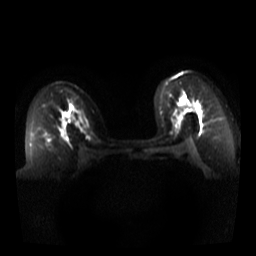
Breast MRI, one axial slice; position 22 of 44 along the scan axis; diffusion-weighted series; image 2 of 4 stored at this slice position (different b-values; order by instance number); 3 T; 5 mm slice thickness; 256 × 256 image matrix, field of view 340 × 340 mm. Female patient.
Structures marked on this image (manually delineated by an expert):
- tumour on diffusion-weighted imaging: box from (x=184, y=100) to (x=199, y=109) px